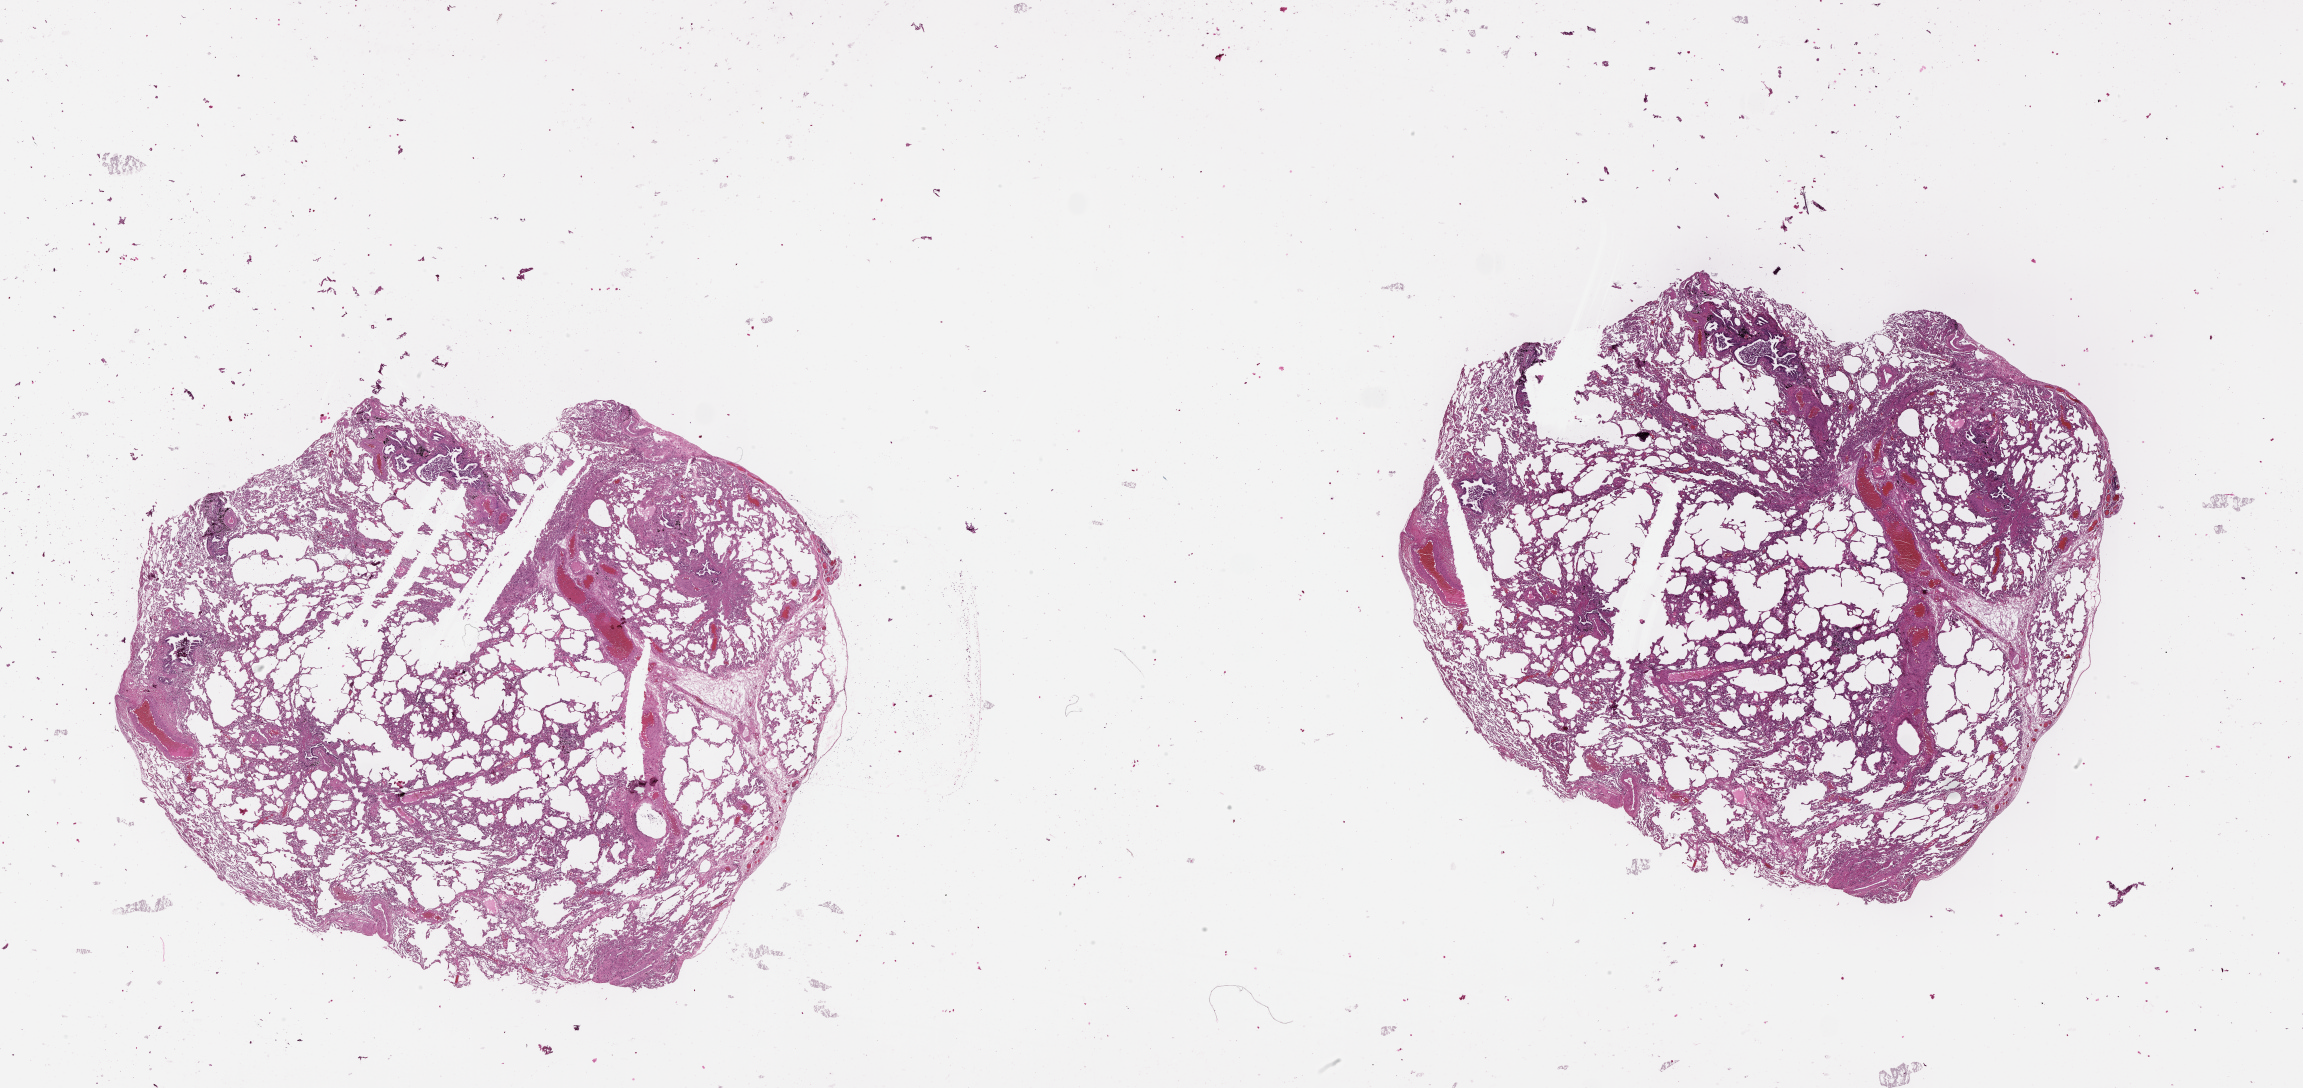
Digitized H&E-stained tissue section (whole slide) — shown as a low-resolution overview of the whole scanned area (about 37.1 x 17.5 mm); normal (non-tumour) tissue sample, lung. Male, 65 y/o.
This section: normal (non-tumour) tissue from the same patient. Patient diagnosis (cohort enrolment): squamous cell carcinoma (lung).